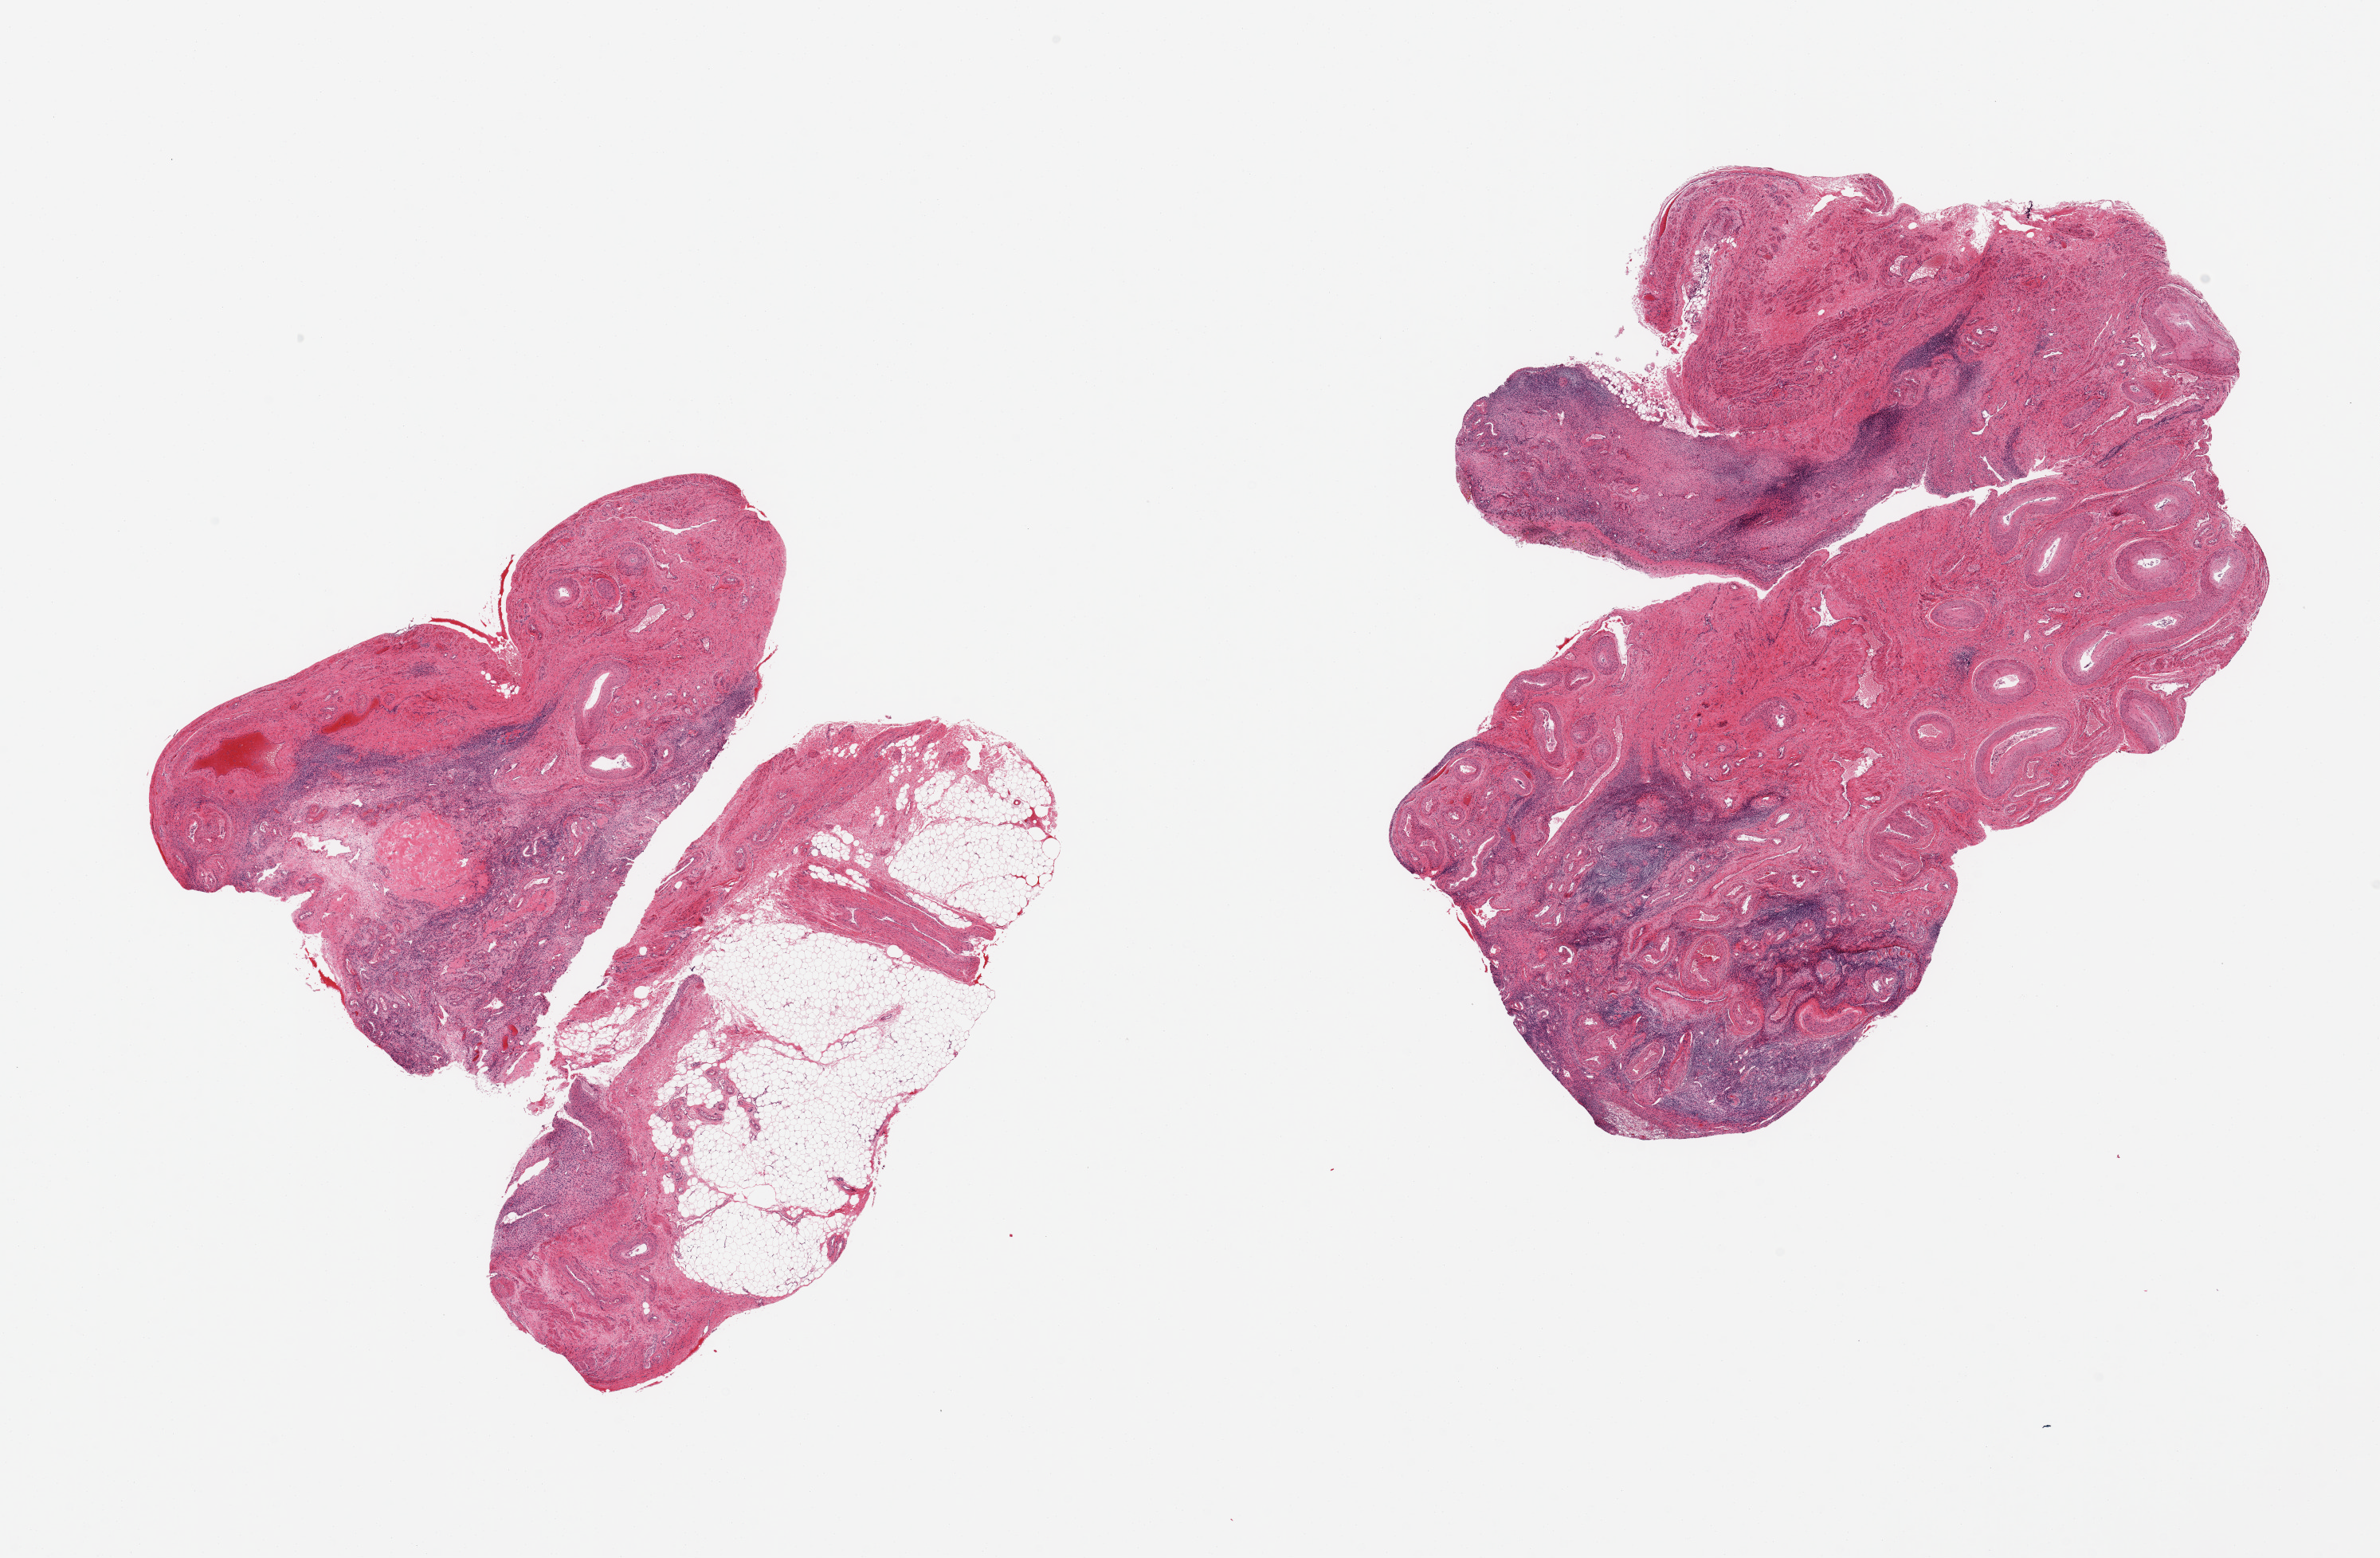
H&E whole-slide image, brightfield, shown as a low-resolution overview of the whole scanned area (about 23.6 x 15.5 mm); PAXgene-fixed paraffin-embedded (PFPE) section; section of ovary (target tissue); donor tissue sample. Donor: female.
Reviewer comment on this tissue sample: 3 pieces, involuted parenchyma; ~25% adherent fibroadipose tissue.